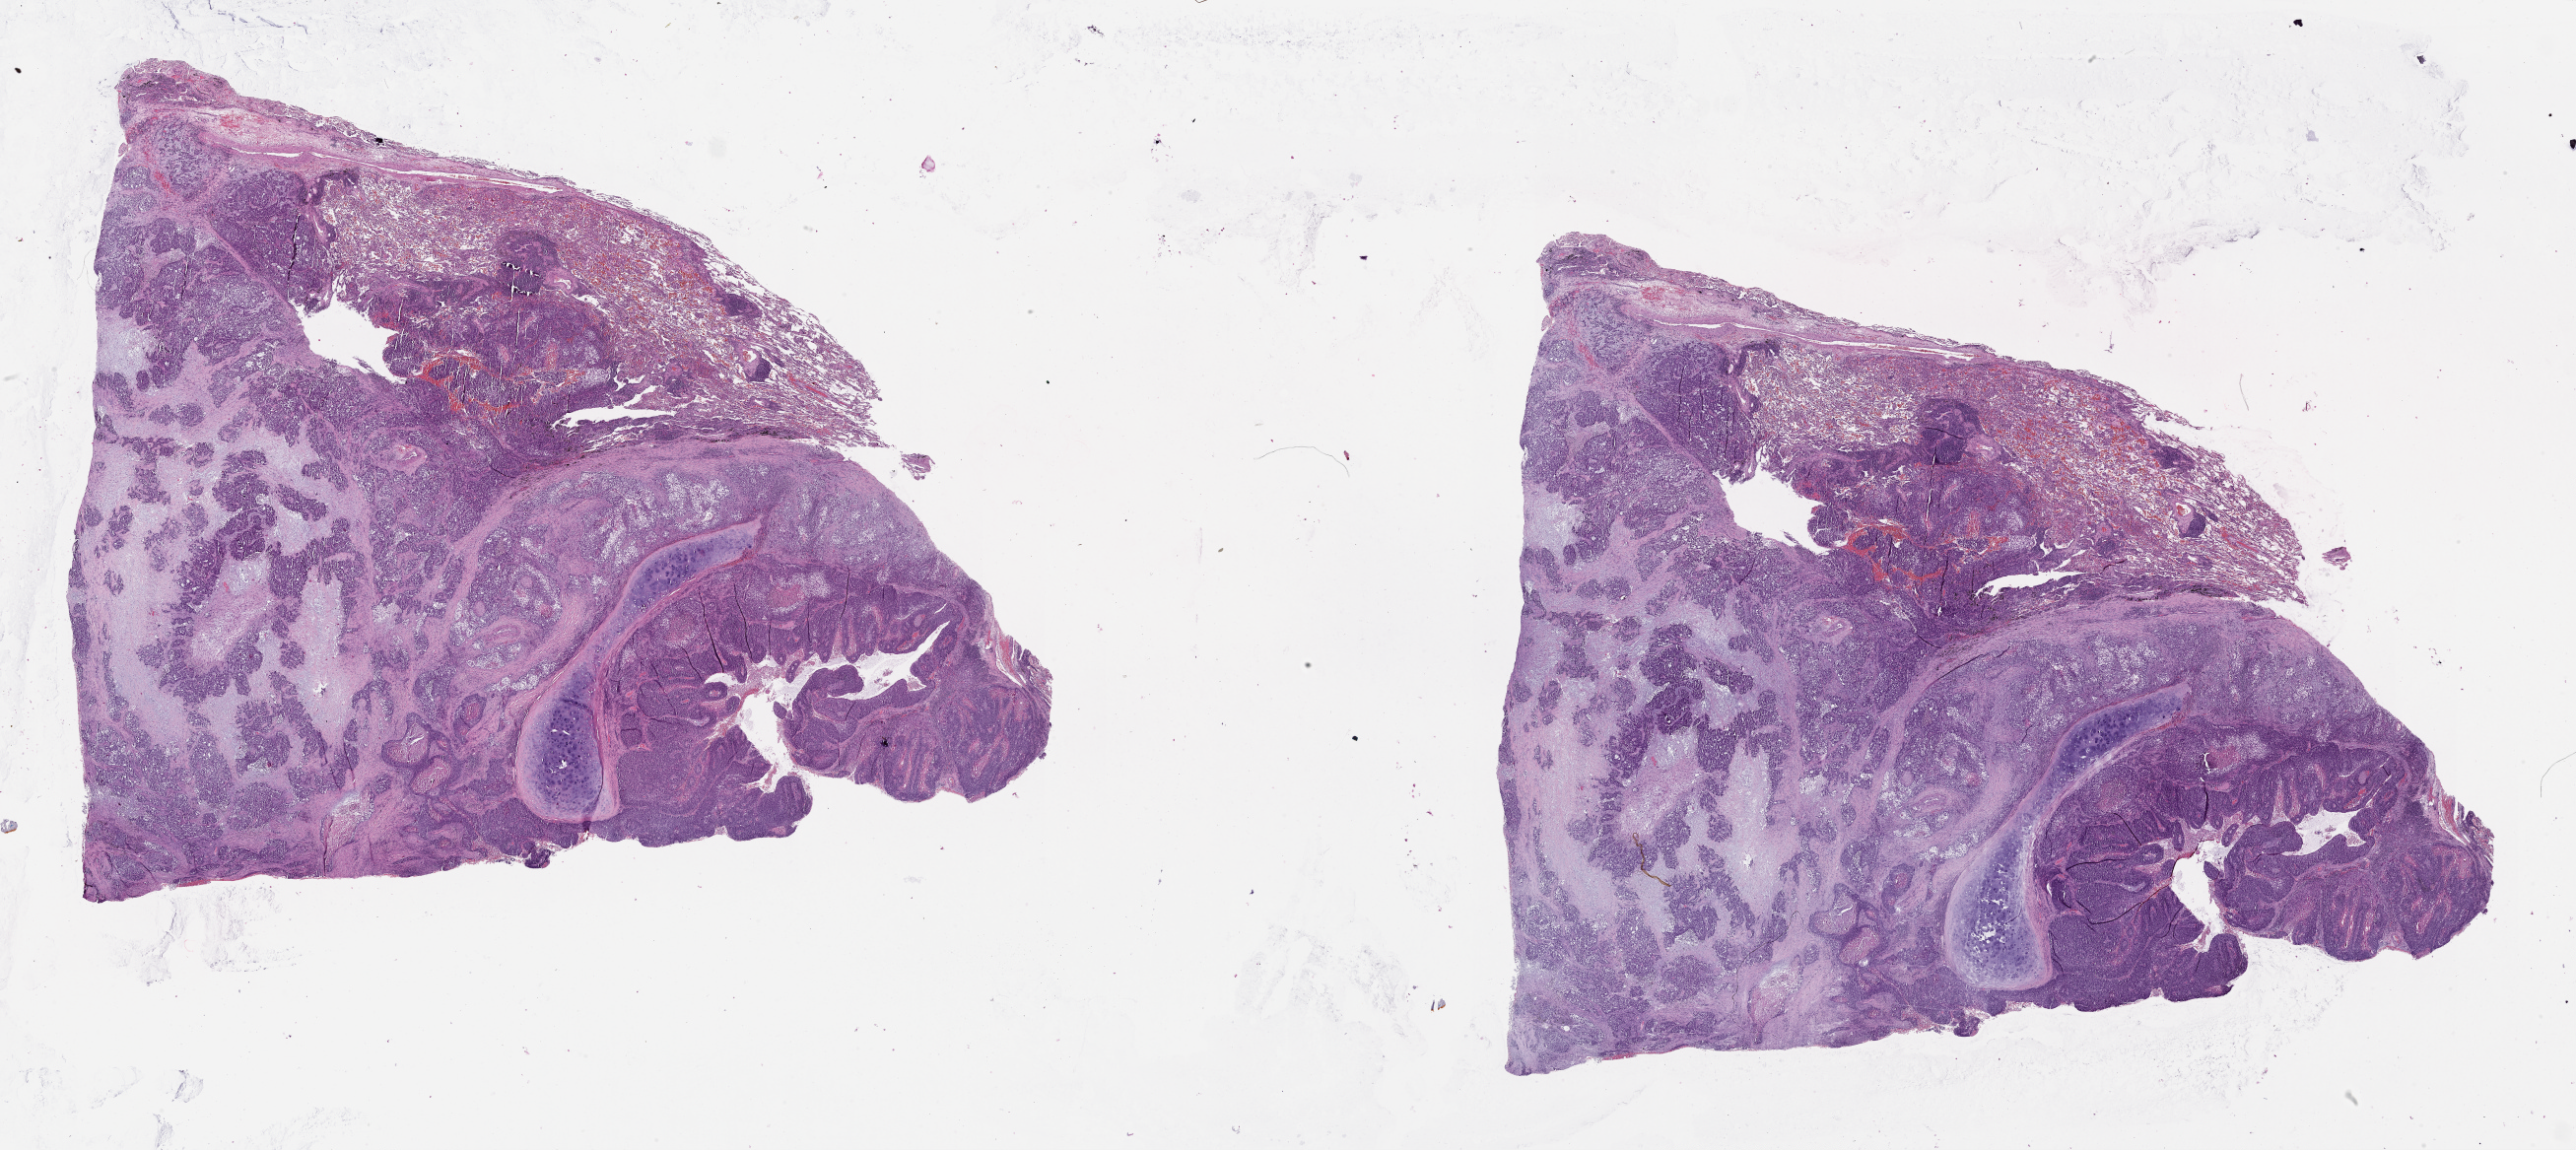
Whole-slide histology image, H&E — whole scanned area (about 42.1 x 18.8 mm) shown as a low-resolution overview; lung, tissue type not recorded.
- patient diagnosis (cohort enrolment): squamous cell carcinoma (lung)